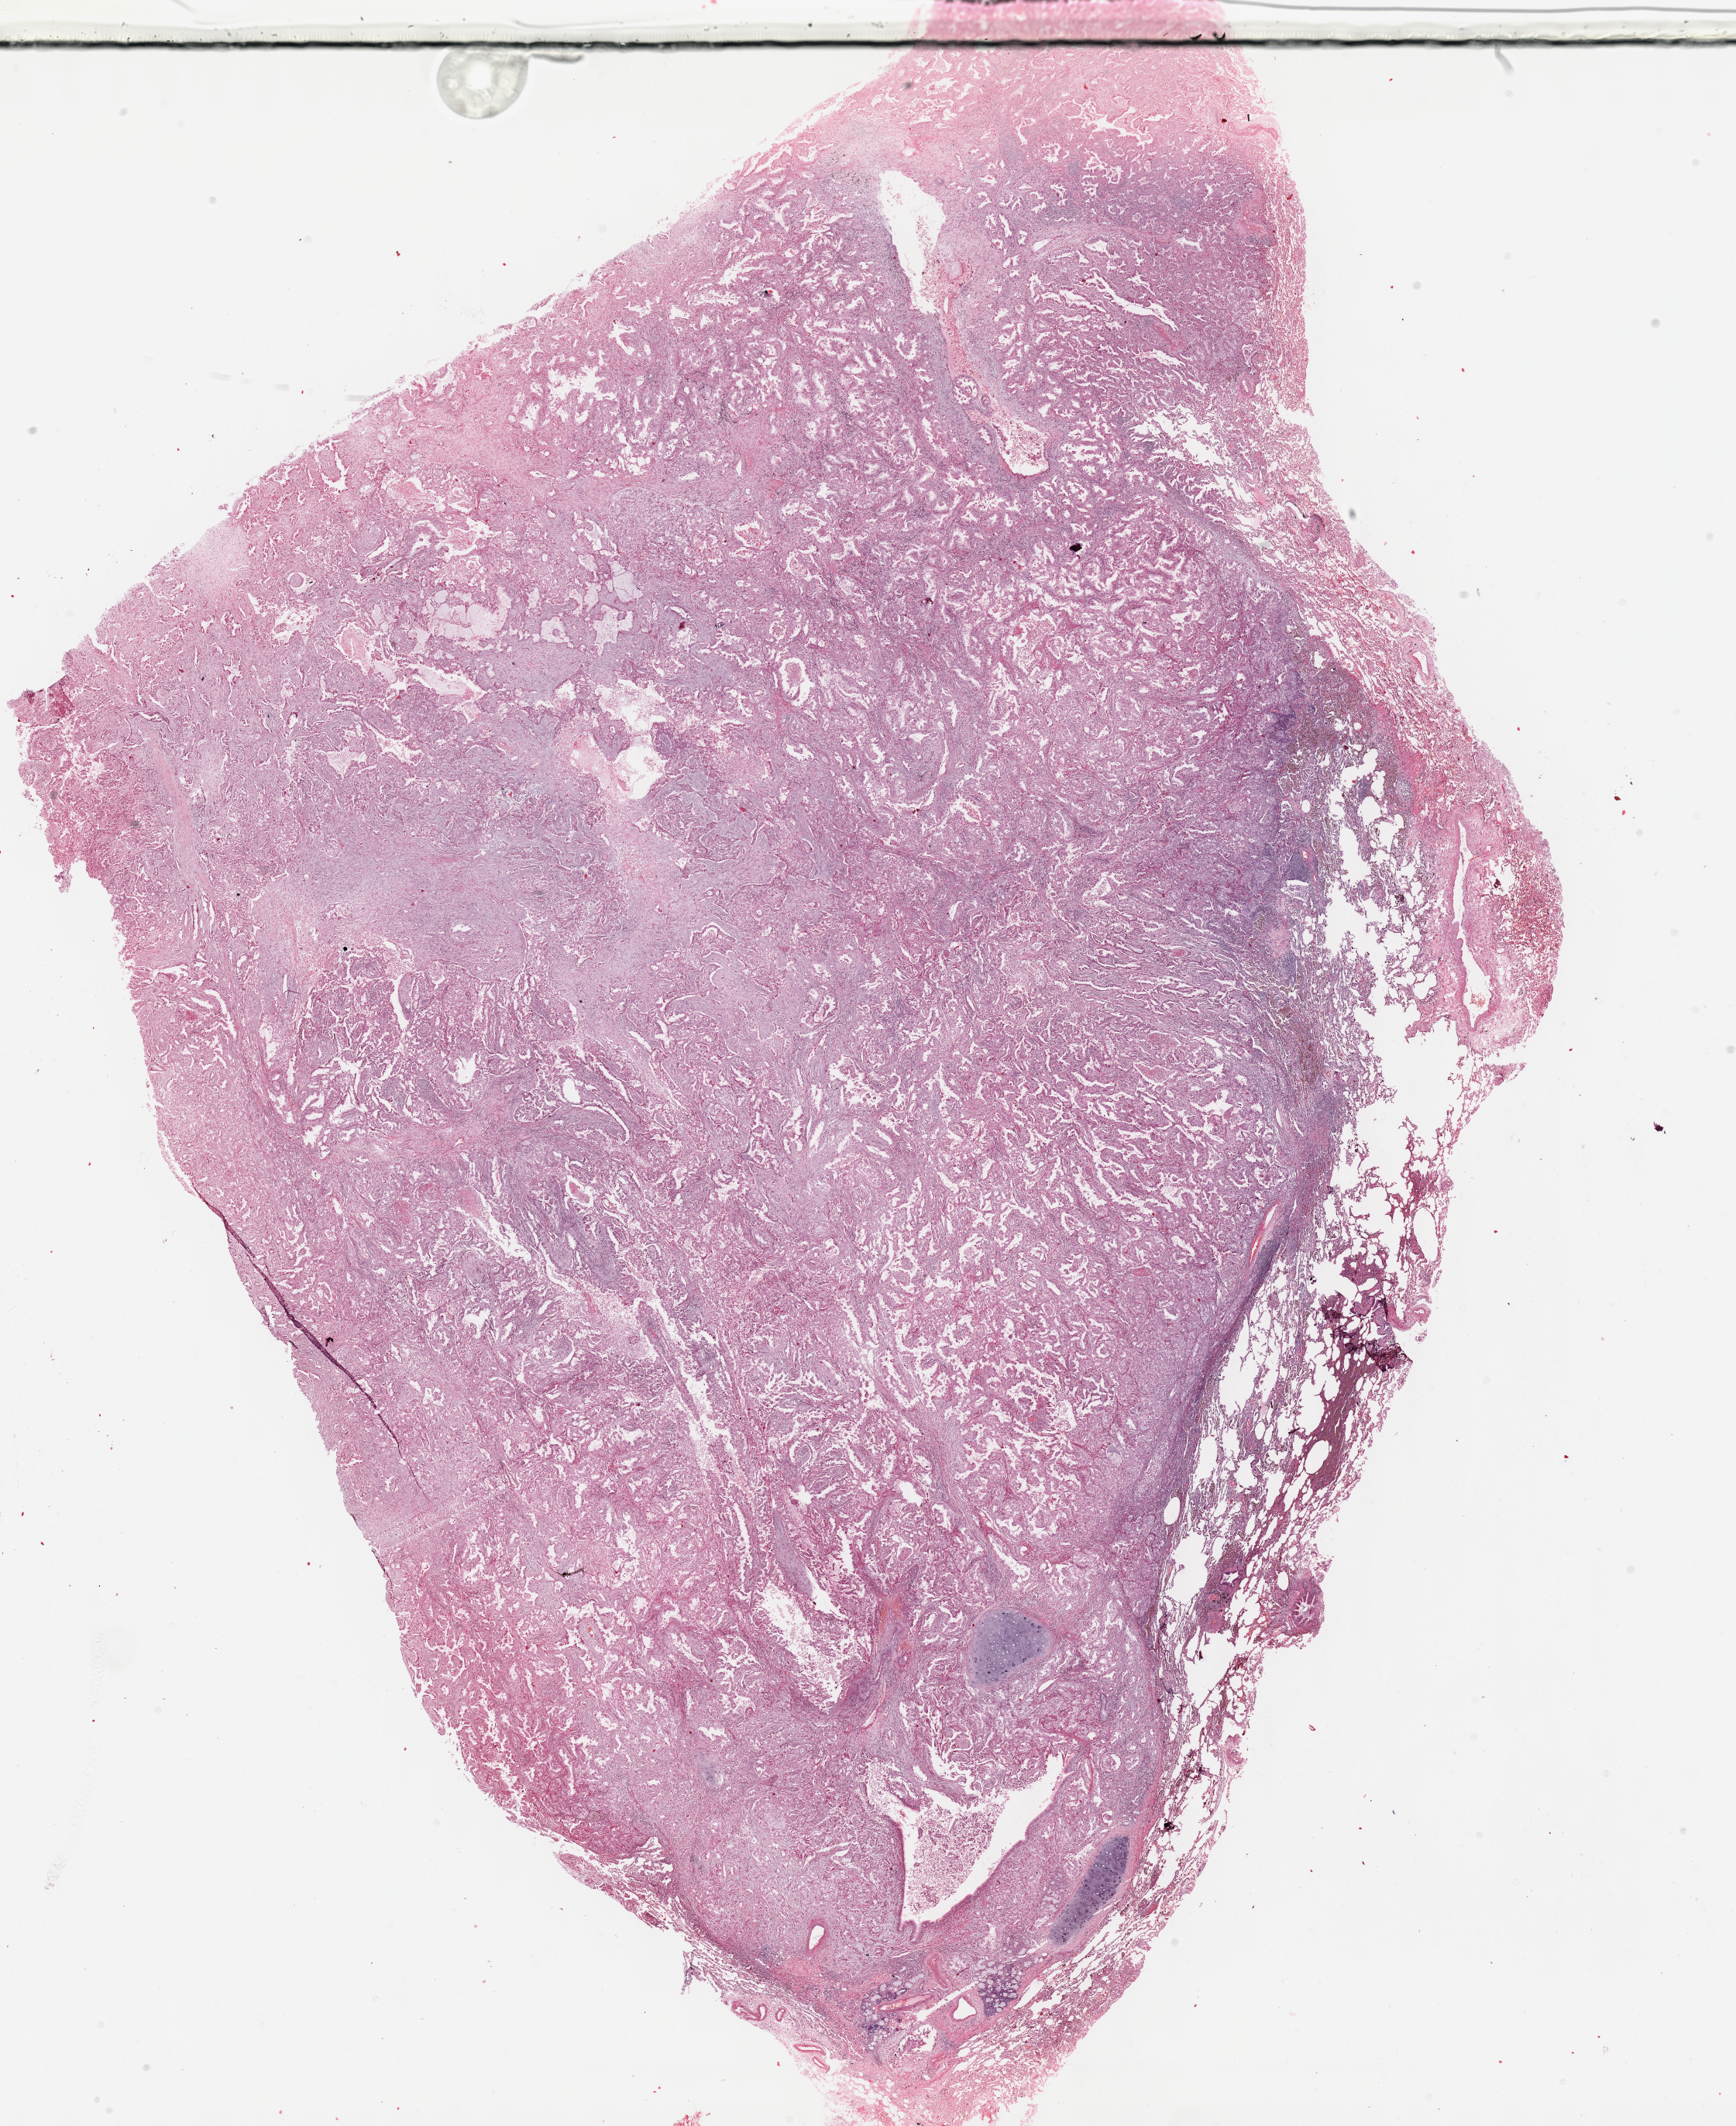
H&E-stained whole-slide image — a low-resolution overview of the entire scanned area, about 18.1 x 22.2 mm. Formalin-fixed paraffin-embedded (FFPE) diagnostic section. Lung, primary tumour sample. Female patient; age at initial diagnosis 60 years.
Diagnosis: Adenocarcinoma, NOS (upper lobe, lung). AJCC pathologic stage: IB.